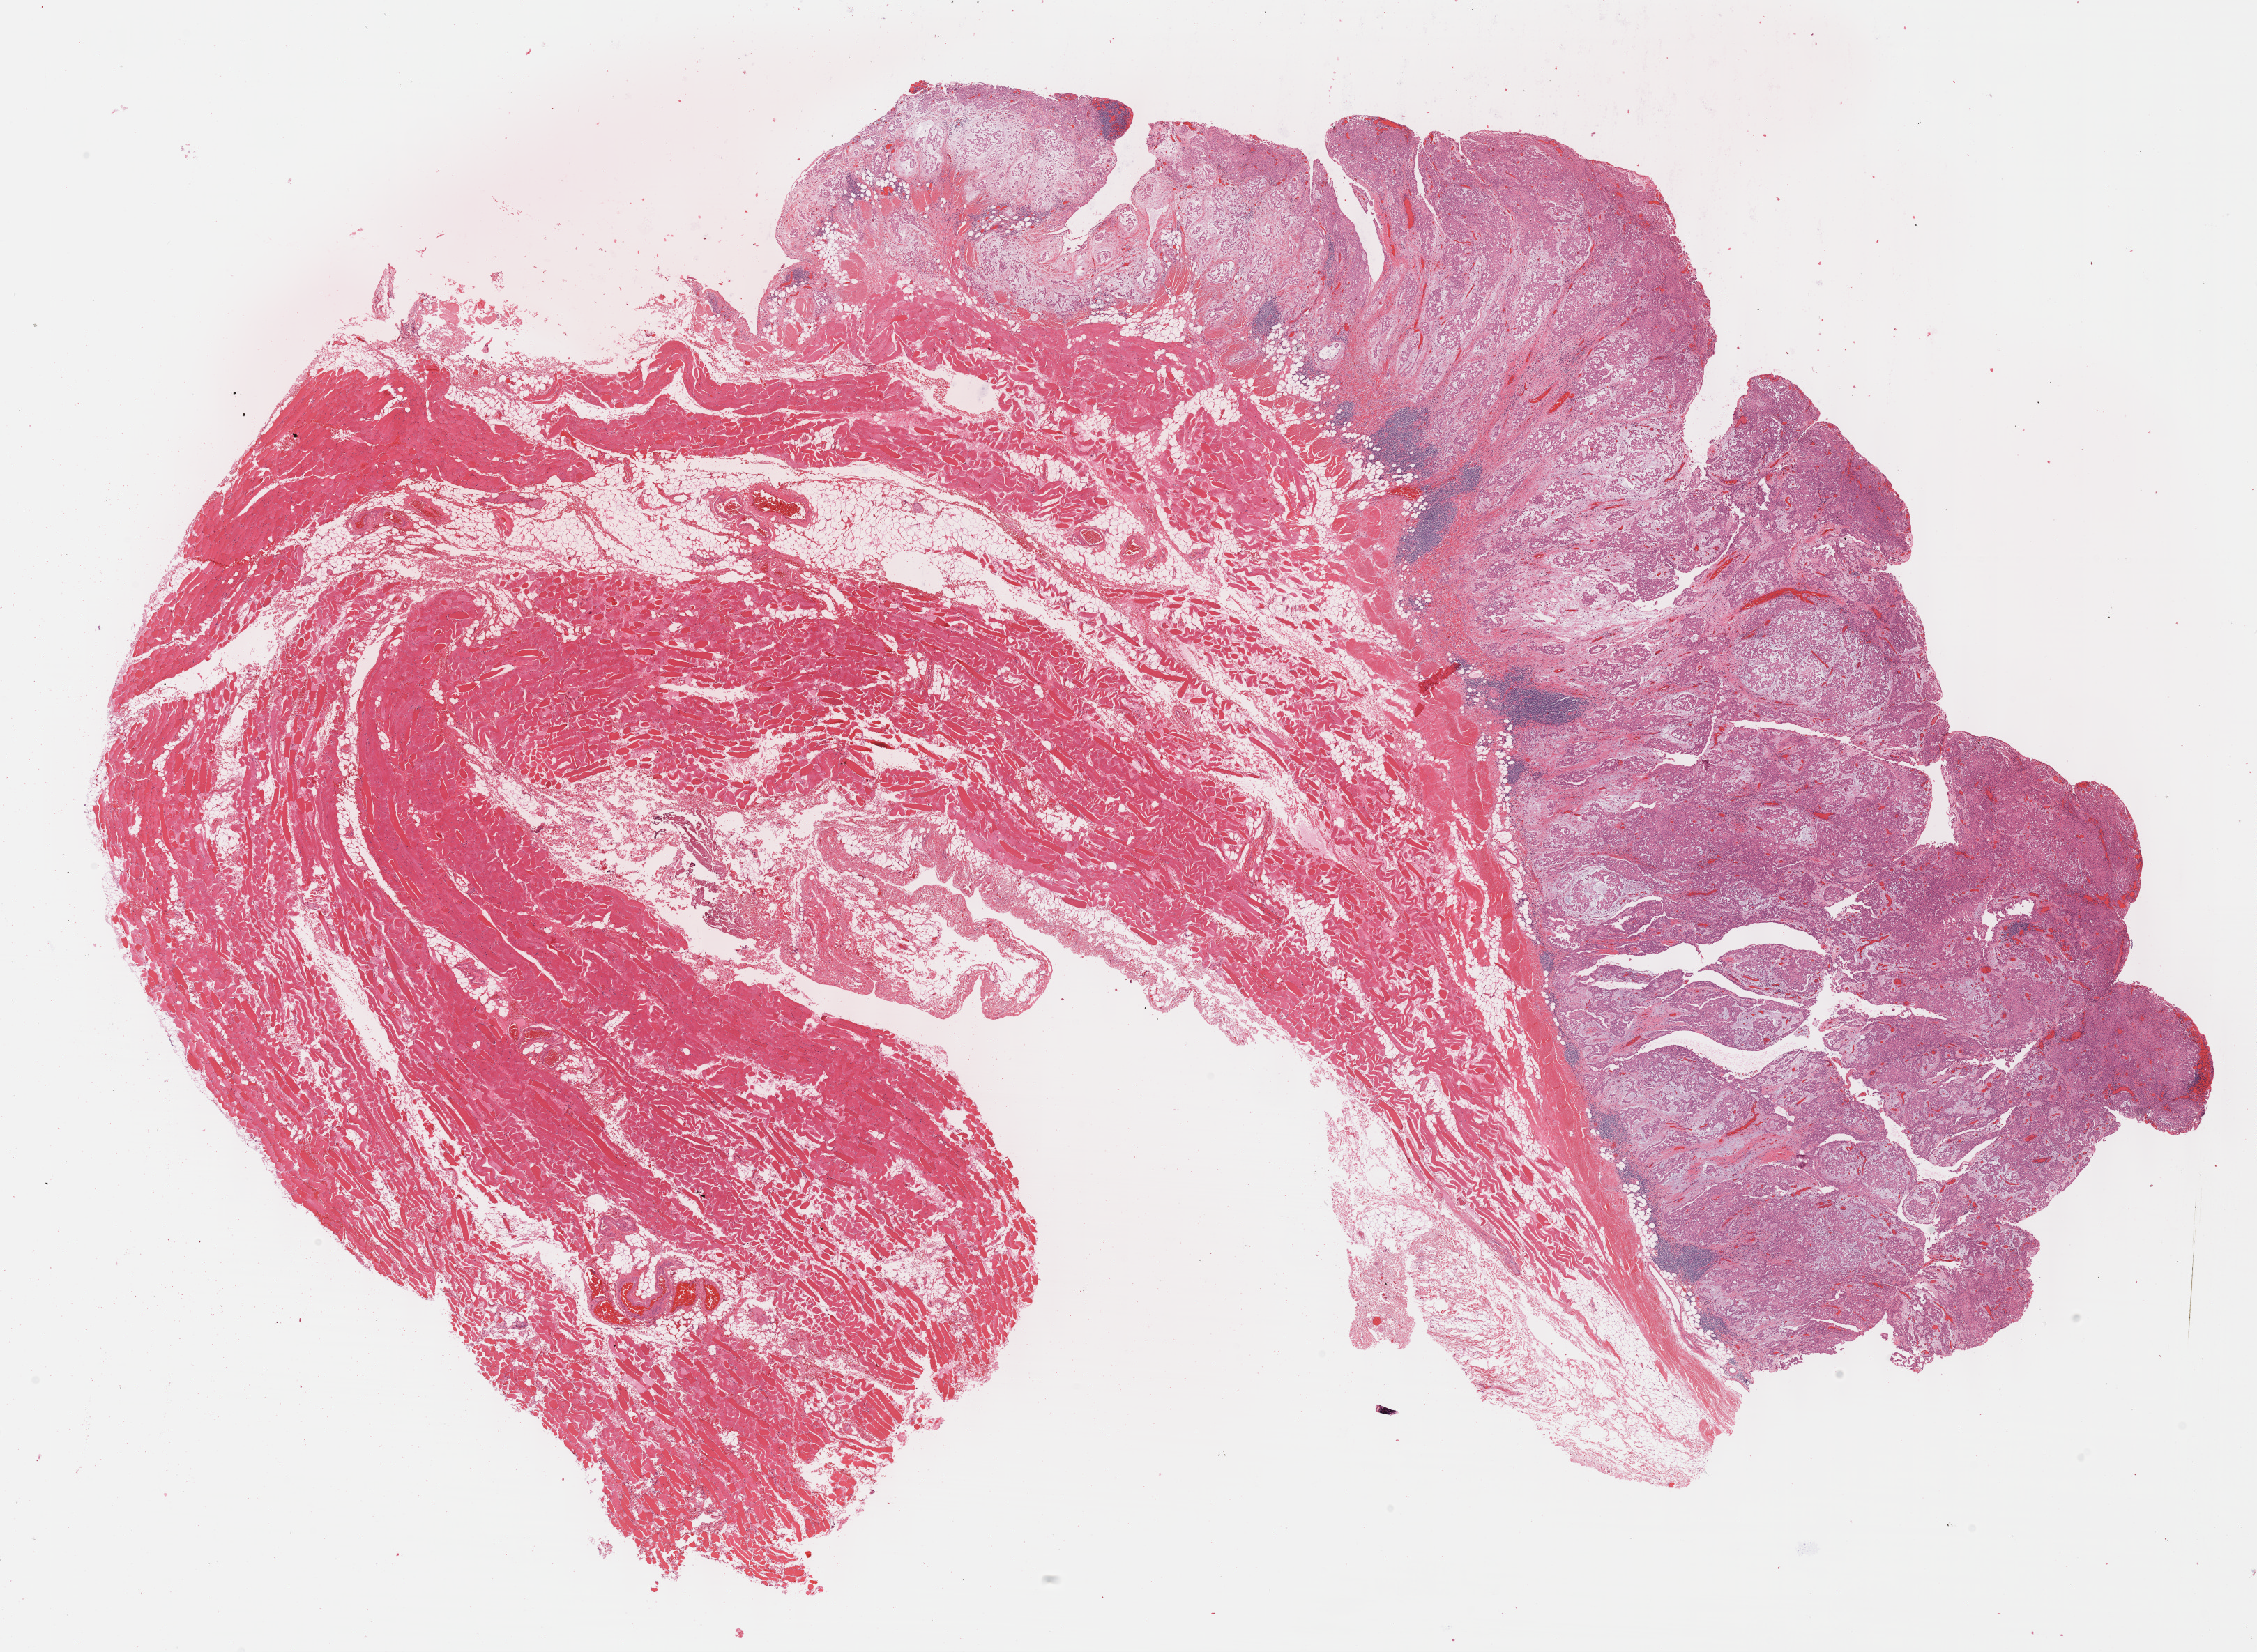
Hematoxylin and eosin (H&E) stained whole-slide image — whole scanned area (about 26.2 x 19.1 mm, acquisition: 40x scan) shown as a low-resolution overview; formalin-fixed paraffin-embedded (FFPE) diagnostic section; sample: primary tumour, mesothelium. Patient: male, age at initial diagnosis 70 years.
• AJCC pathologic stage: II
• diagnosis: Epithelioid mesothelioma, malignant (pleura, NOS)